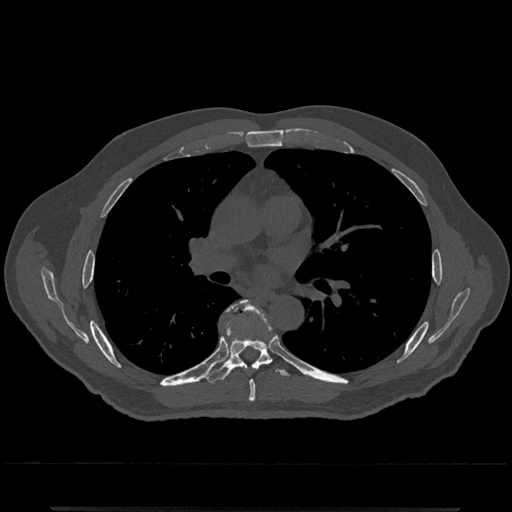
CT including the spine, one axial slice. Position 743 of 797 along the scan axis. Reconstruction kernel Br40s/3. Bone window (W 1800 / L 400 HU). 0.5 mm slice thickness. 512 × 512 image matrix, field of view 393 × 393 mm. Male patient, age 67 years. From the clinical record (not read from this slice): primary cancer: prostate.
Annotated regions visible in this slice (semi-automatically segmented with operator editing):
- T6 vertebra: bounding box <228,300,256,402> (left, top, right, bottom; pixels)
- T7 vertebra: <204,304,291,385>